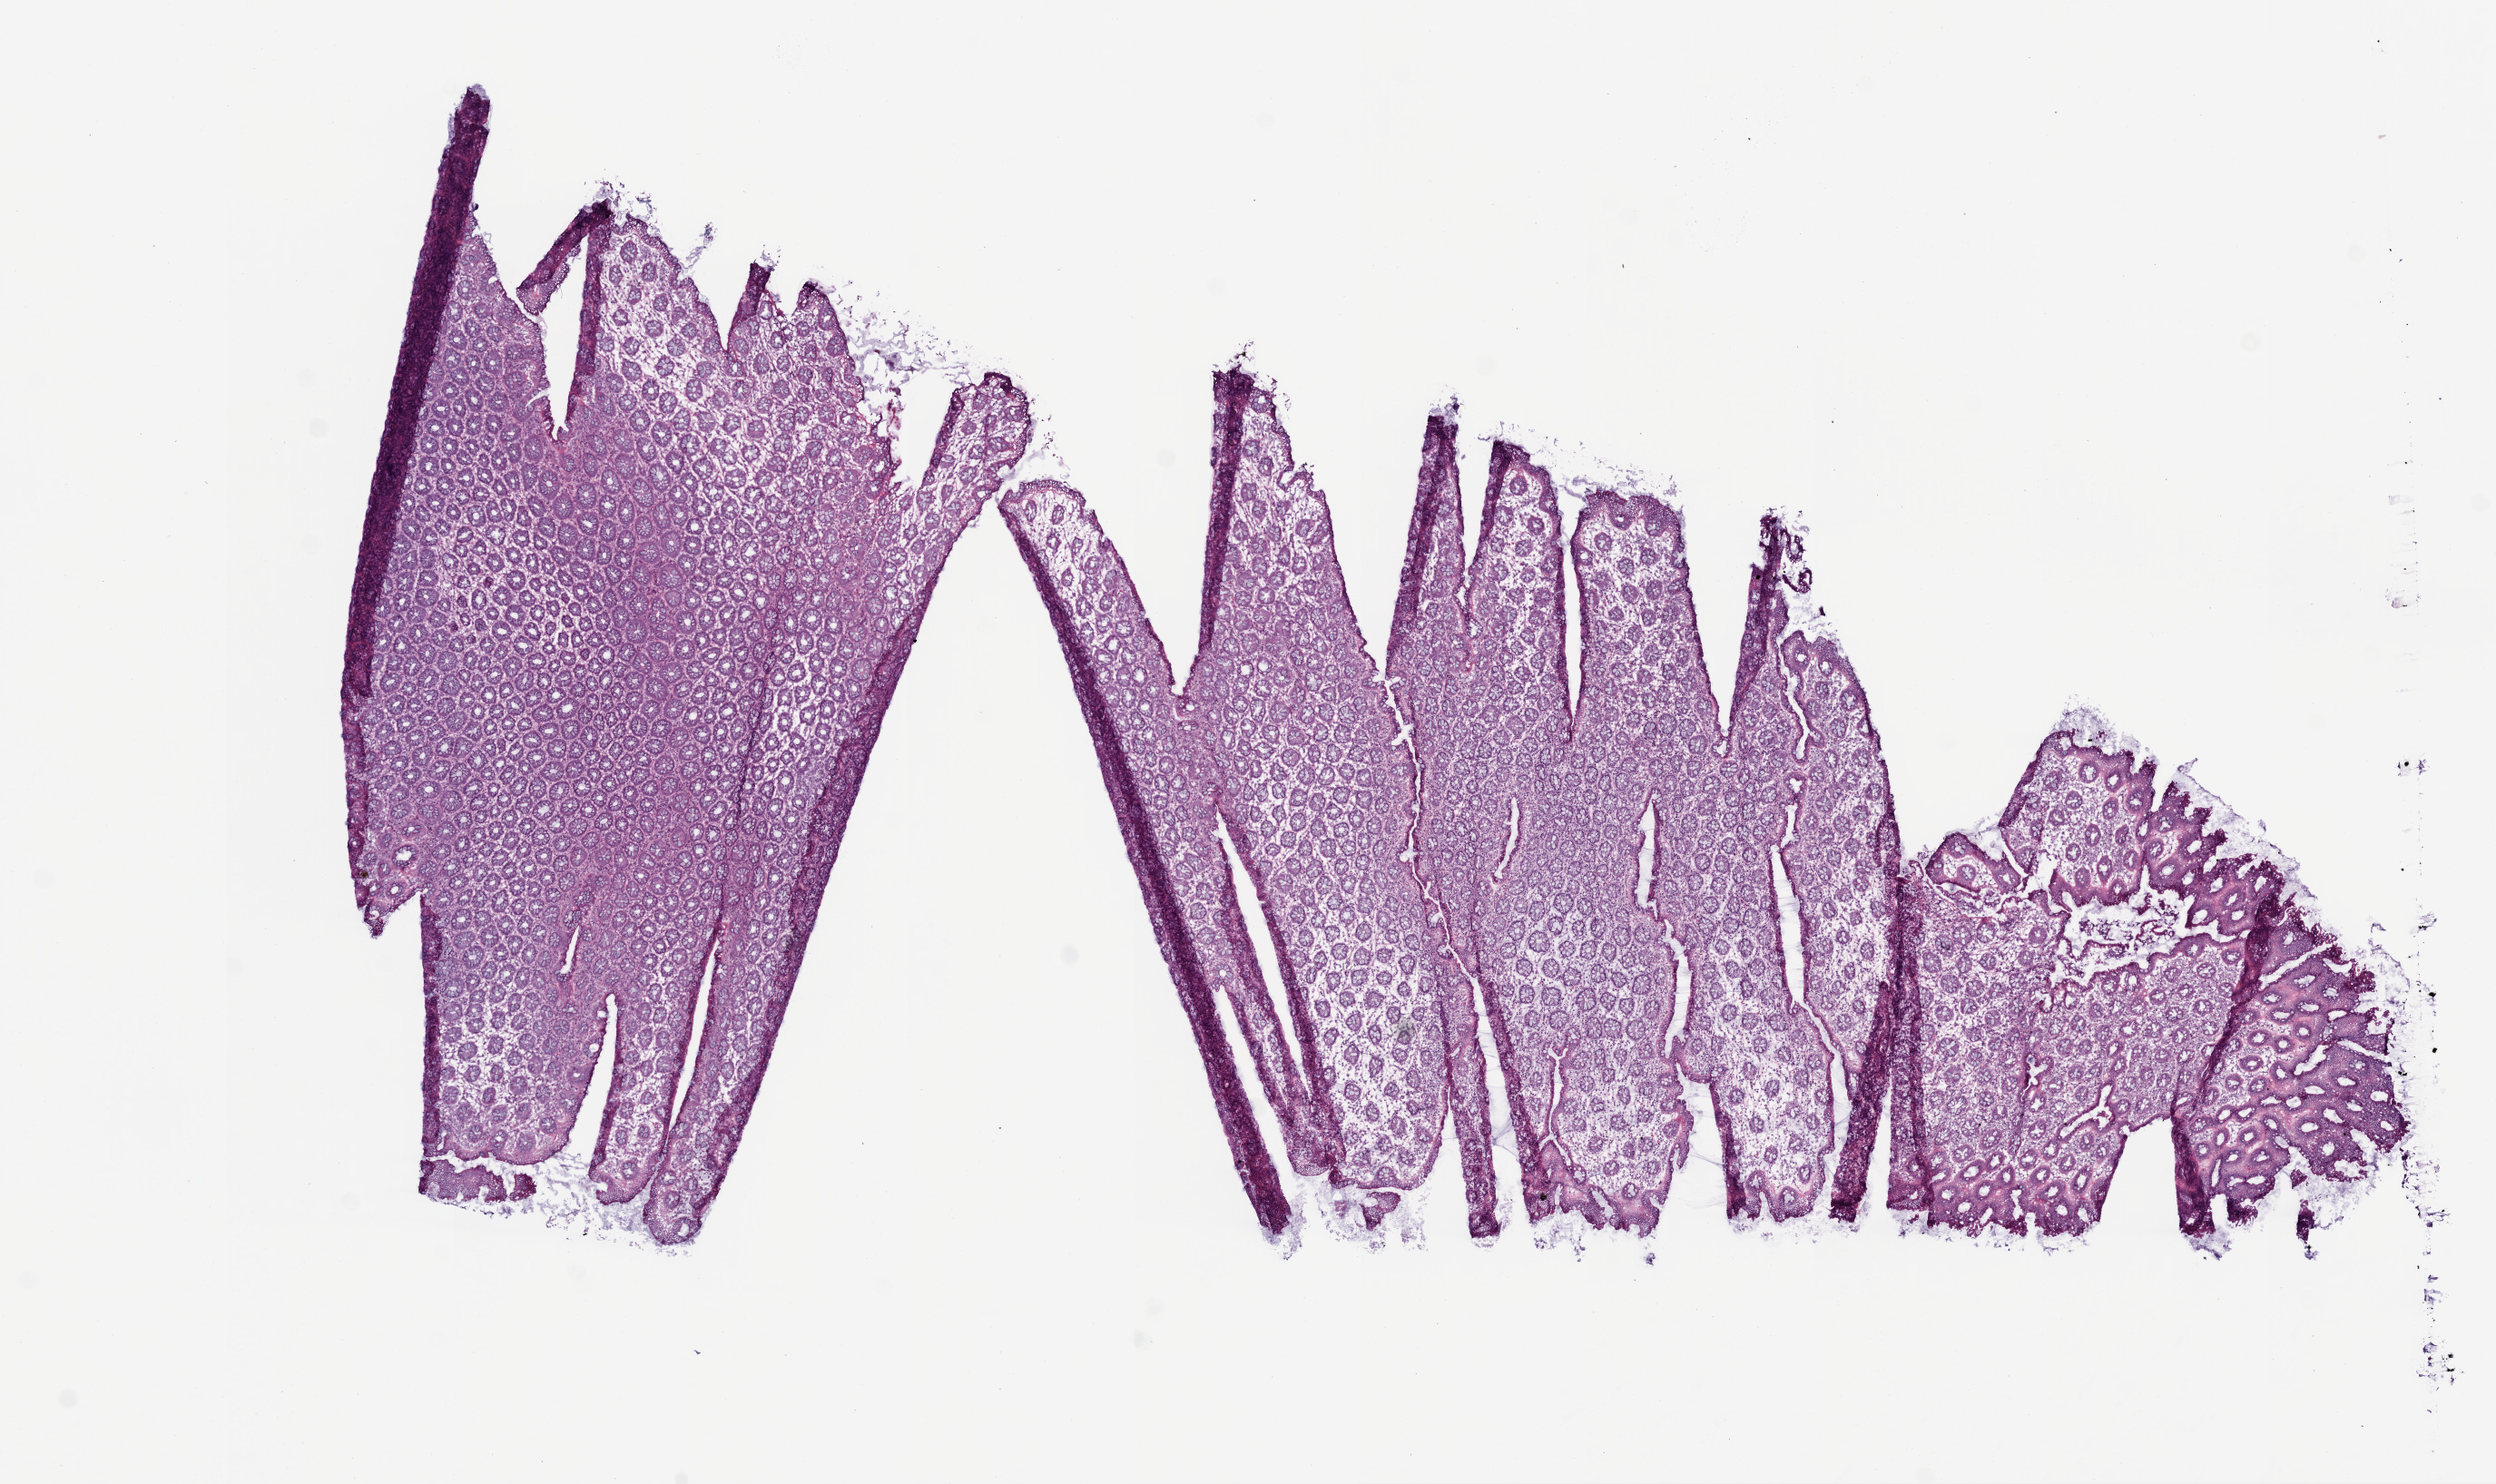
H&E whole-slide image — shown as a low-resolution overview of the whole scanned area (about 11.0 x 6.6 mm); frozen section from the top of the tissue portion; sample: solid tissue normal (non-tumour tissue), colon. Male patient; age at initial diagnosis 65 years.
This section: solid tissue normal sample (biorepository sample class). Patient diagnosis: Adenocarcinoma, NOS (descending colon).